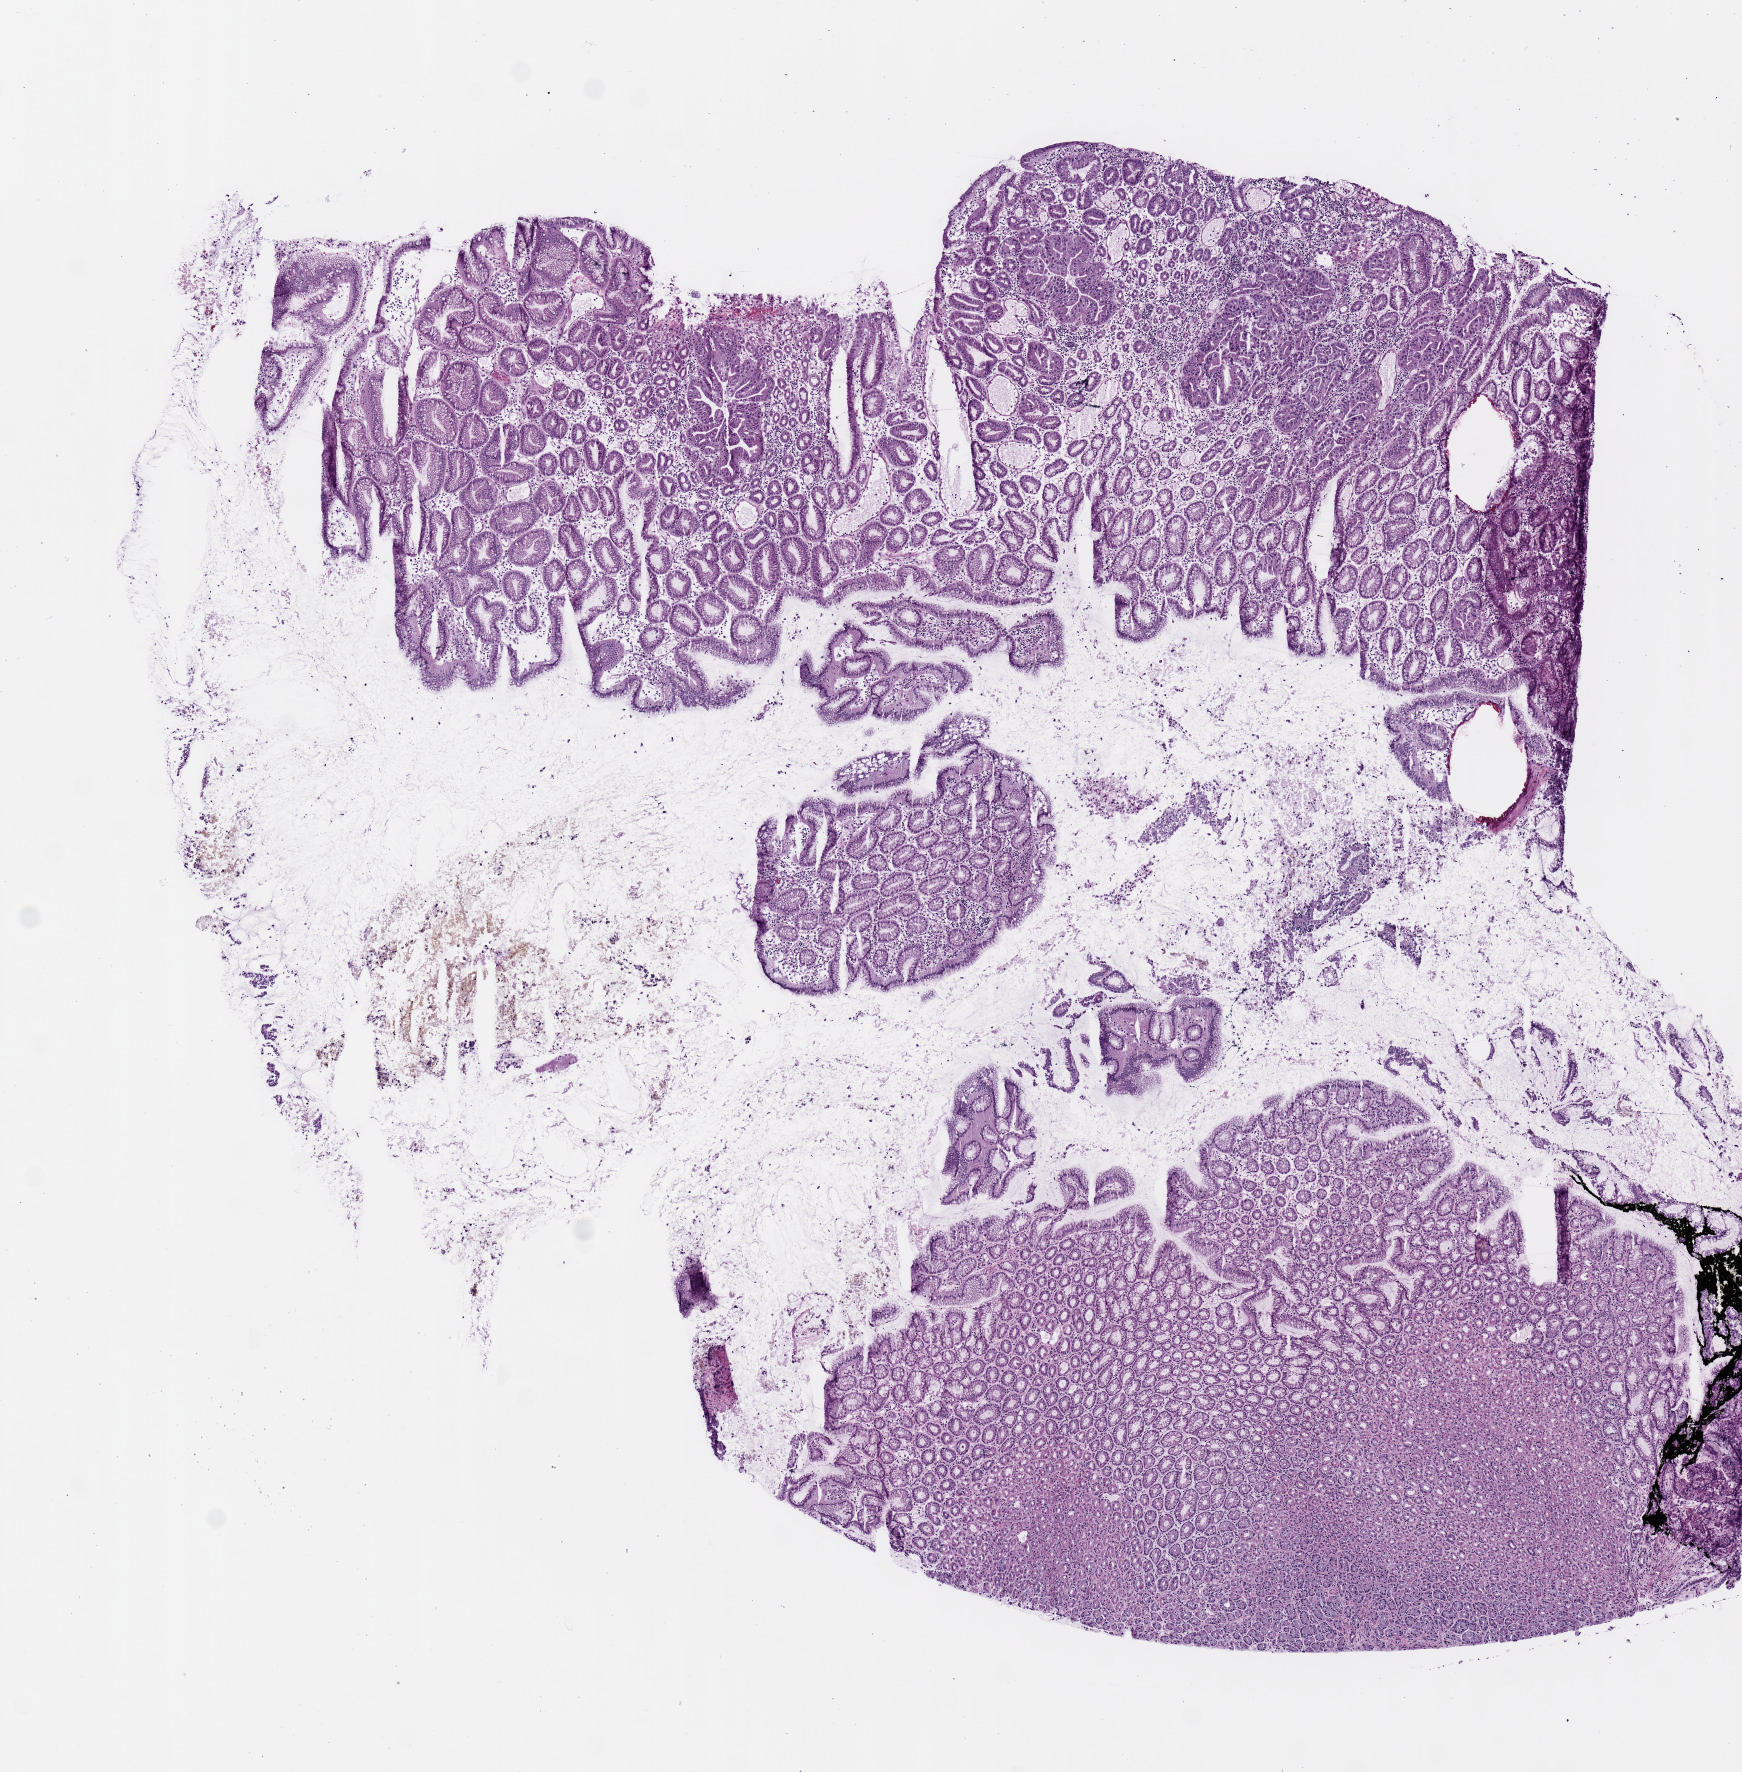
H&E-stained whole-slide image, shown as a low-resolution overview of the whole scanned area (about 6.9 x 7.0 mm, from a 20x scan), frozen section from the top of the tissue portion, primary tumour sample from the stomach. Male patient; age at initial diagnosis 62 years. Slide review estimates, as recorded: tumour cells 73%, tumour nuclei 60%.
Histologic diagnosis: Adenocarcinoma, NOS (cardia, NOS).